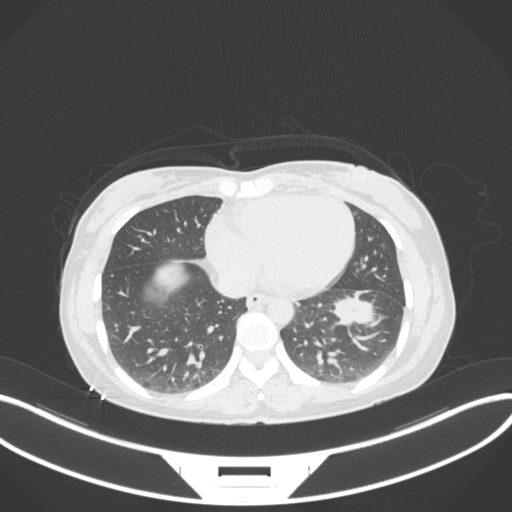
Chest CT, one axial slice; position 123 of 361 along the scan axis; reconstruction kernel B31f; 120 kVp; lung window (W 1500 / L -600 HU); 1 mm slice thickness; 512 × 512 image matrix. Female patient, age 41 years. Case-level facts recorded for this patient, not image findings: clinical TNM (as recorded): T2a N3 M1b.
Structures marked on this image (rectangle marked by the reading radiologist):
- lung tumour (recorded histology: adenocarcinoma): bounding box [x1, y1, x2, y2] px = [332, 292, 387, 332]